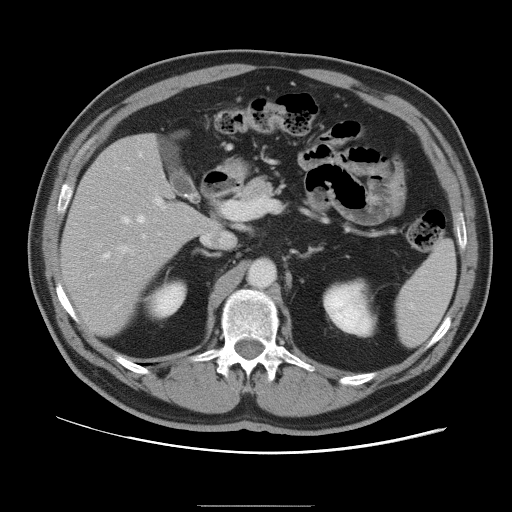
Contrast-enhanced abdominal CT, one axial slice; position 55 of 105 along the scan axis; soft-tissue window (W 400 / L 40 HU); 5 mm slice thickness; 512 × 512 image matrix, field of view 399 × 399 mm. Male patient, age 64 years. Case-level facts recorded for this patient, not image findings: diagnosis: colorectal cancer liver metastases, imaged before liver resection; multiple liver metastases: yes; largest metastasis: 3 cm; chemotherapy before resection: yes.
Annotated regions visible in this slice (manually delineated by an expert):
- hepatic veins: bounding box <103,167,145,258> (left, top, right, bottom; pixels)
- liver: <63,135,214,335>
- planned liver remnant (the part of the liver to remain after resection): <63,135,215,335>
- portal vein (with intrahepatic branches): <118,196,166,253>